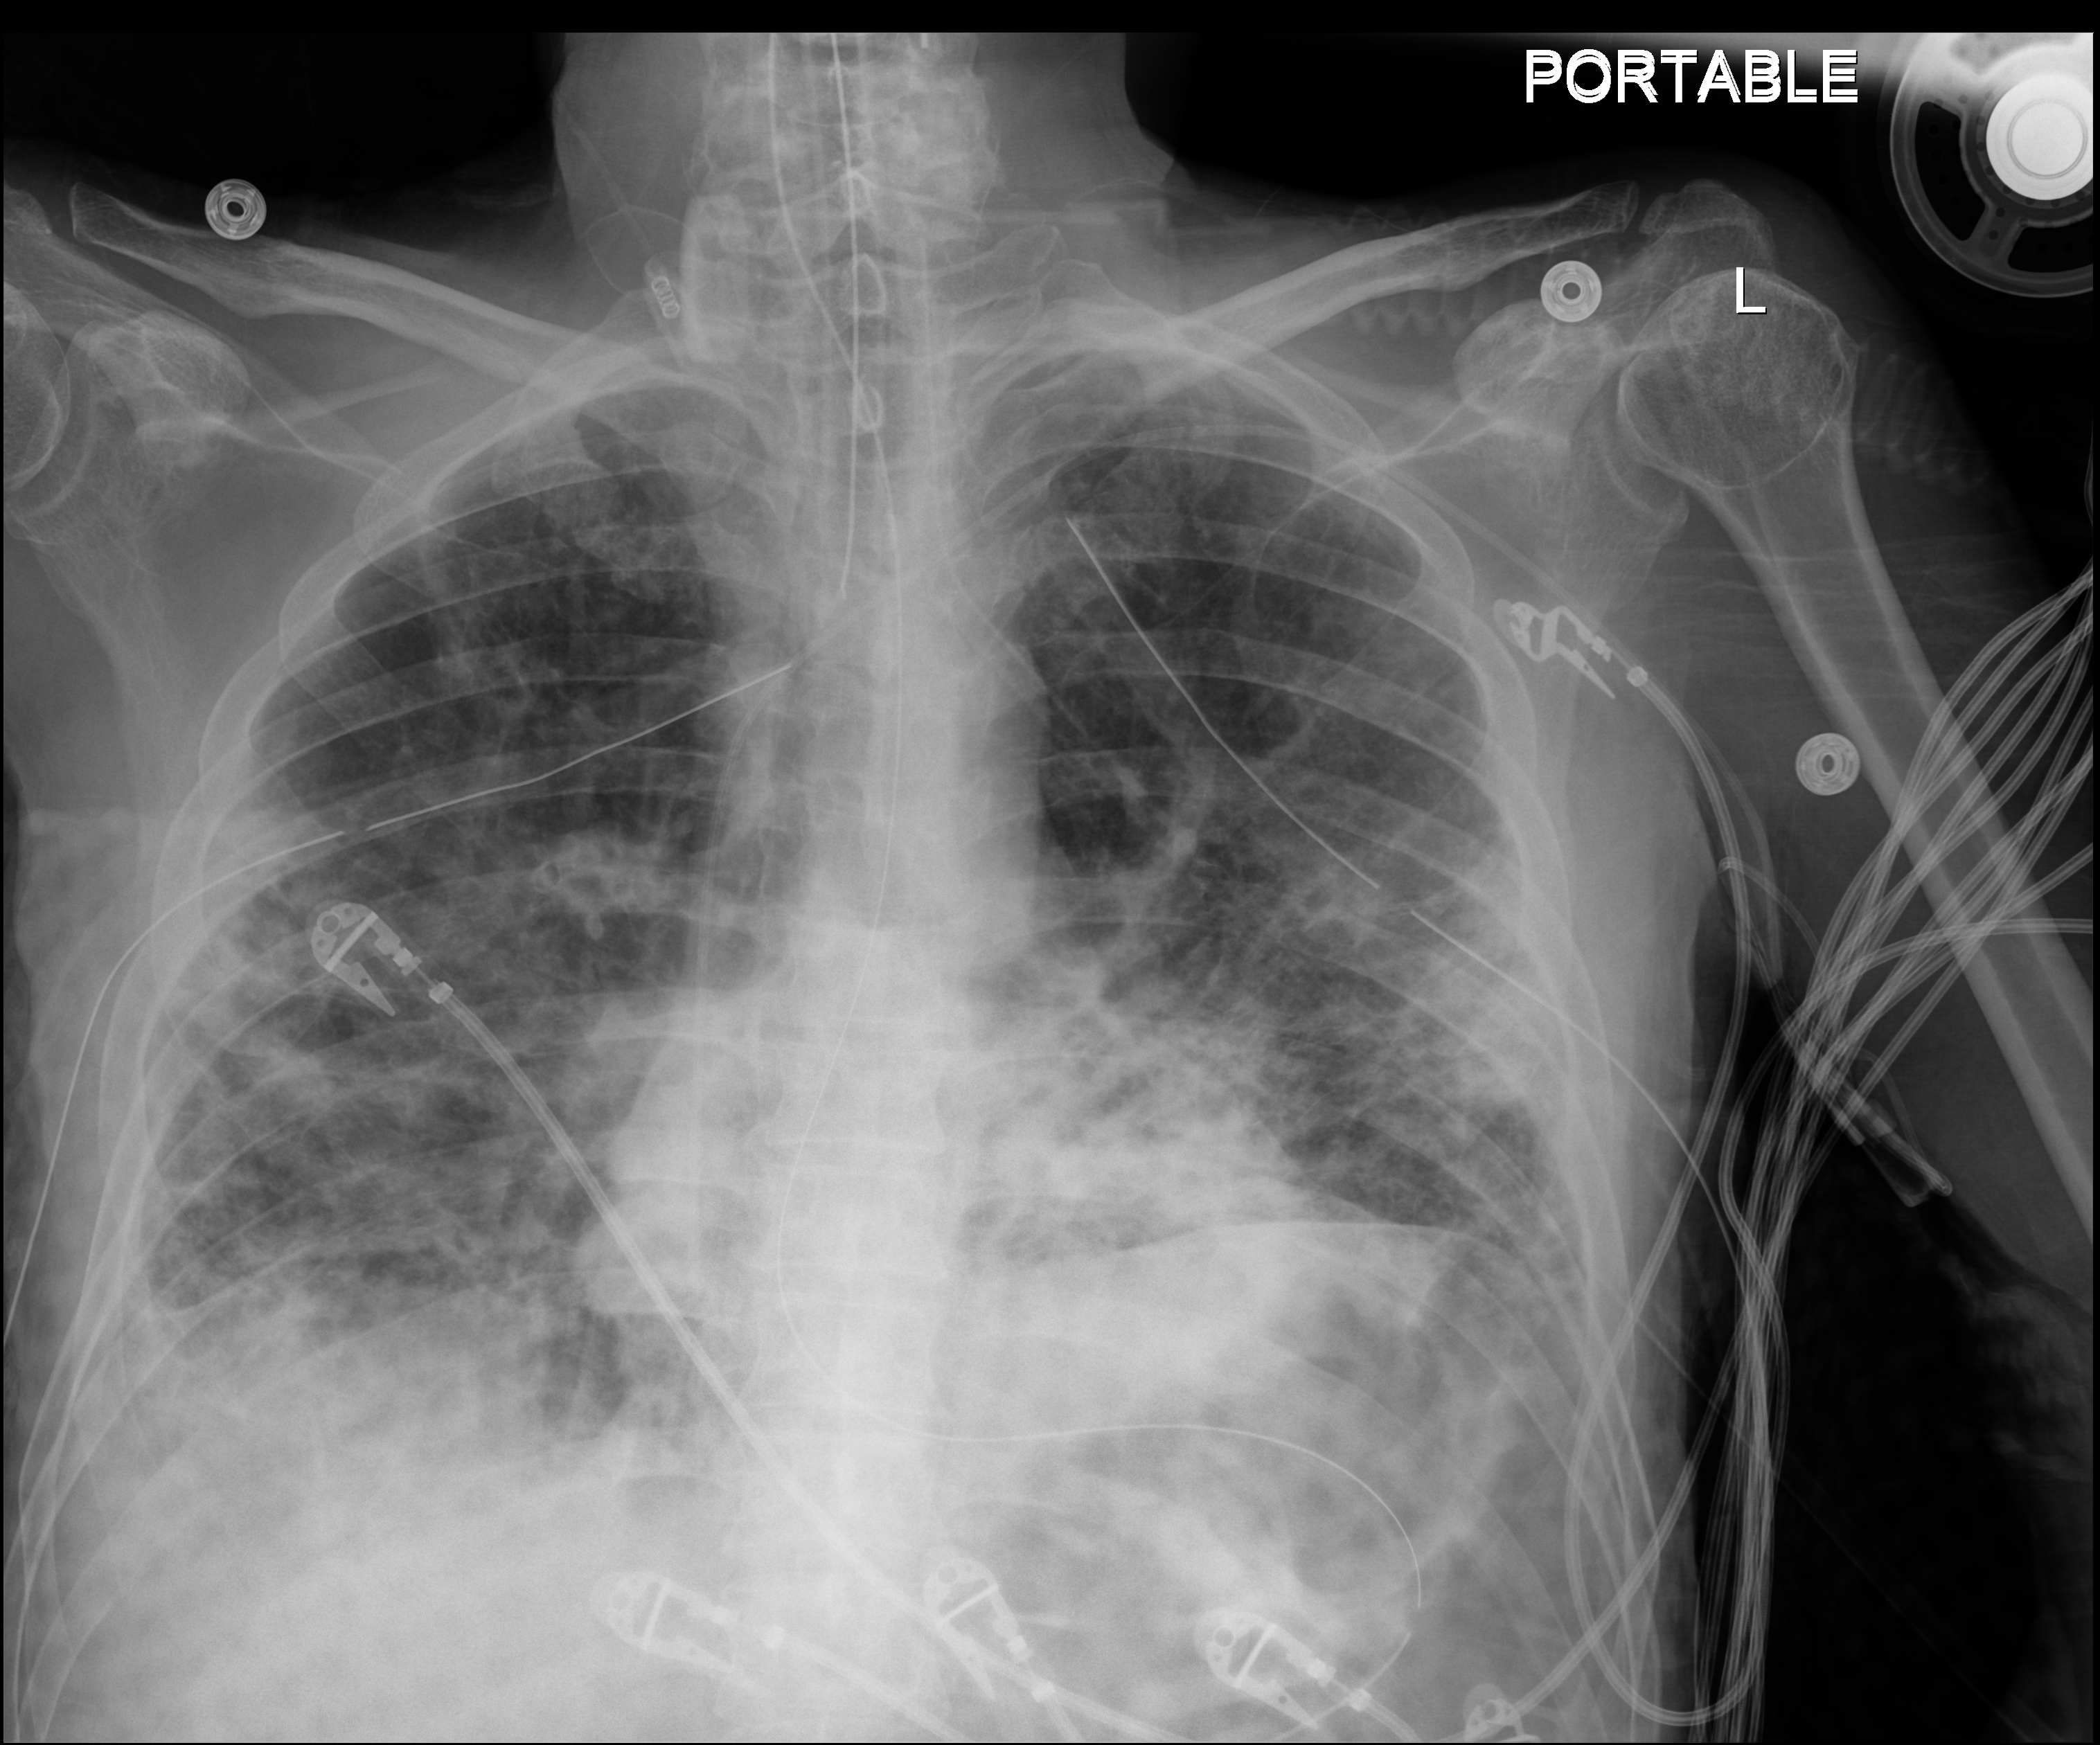
Portable chest radiograph, anteroposterior (AP) projection. Male patient hospitalised with COVID-19, age 18–59 years.
From the hospital-stay record, not from the radiograph (when in the stay this image was taken is not recorded):
- length of hospital stay: 96 days
- diabetes (admission record): yes